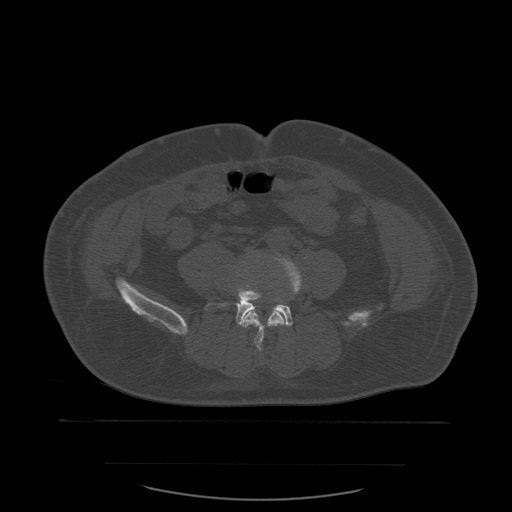
CT including the spine, one axial slice; position 151 of 590 along the scan axis; bone window (W 1800 / L 400 HU); 1.25 mm slice thickness; 512 × 512 image matrix, field of view 479 × 479 mm. Patient age 71 years. Case-level facts recorded for this patient, not image findings: primary cancer: lung.
Annotated regions visible in this slice (semi-automatic segmentation, software-assisted and operator-edited):
- L4 vertebra: bounding box [x1, y1, x2, y2] px = [243, 256, 302, 351]
- L5 vertebra: [205, 282, 293, 327]